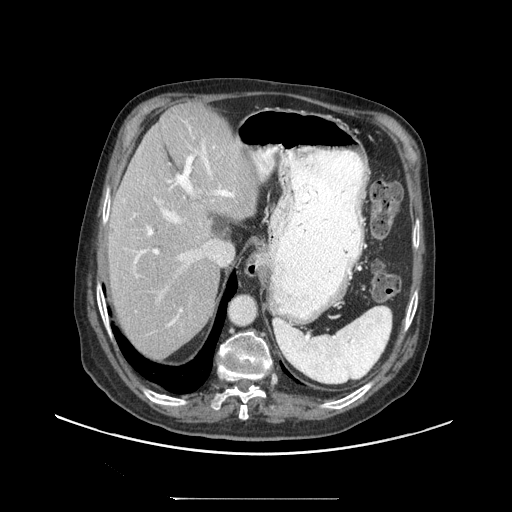
Contrast-enhanced abdominal CT (liver protocol), one axial slice. Position 72 of 97 along the scan axis. 140 kVp. Soft-tissue window (W 400 / L 40 HU). 2.5 mm slice thickness. 512 × 512 image matrix, field of view 450 × 450 mm. Case-level facts recorded for this patient, not image findings: diagnosis: hepatocellular carcinoma (patient treated with transarterial chemoembolisation; whether this scan precedes or follows treatment is not stated here); TNM stage (as recorded): Stage-IIIC; Child-Pugh class: A; tumour differentiation: well differentiated; tumour nodularity: uninodular.
Annotated regions visible in this slice (semi-automatically segmented with operator editing):
- abdominal aorta: bounding box (x1, y1, x2, y2) in pixels: (230, 297, 256, 325)
- liver parenchyma outside the tumour (the mass and vessels are separate outlines, so this box may not span the whole liver): (108, 102, 260, 356)
- liver vessels: (134, 144, 235, 326)